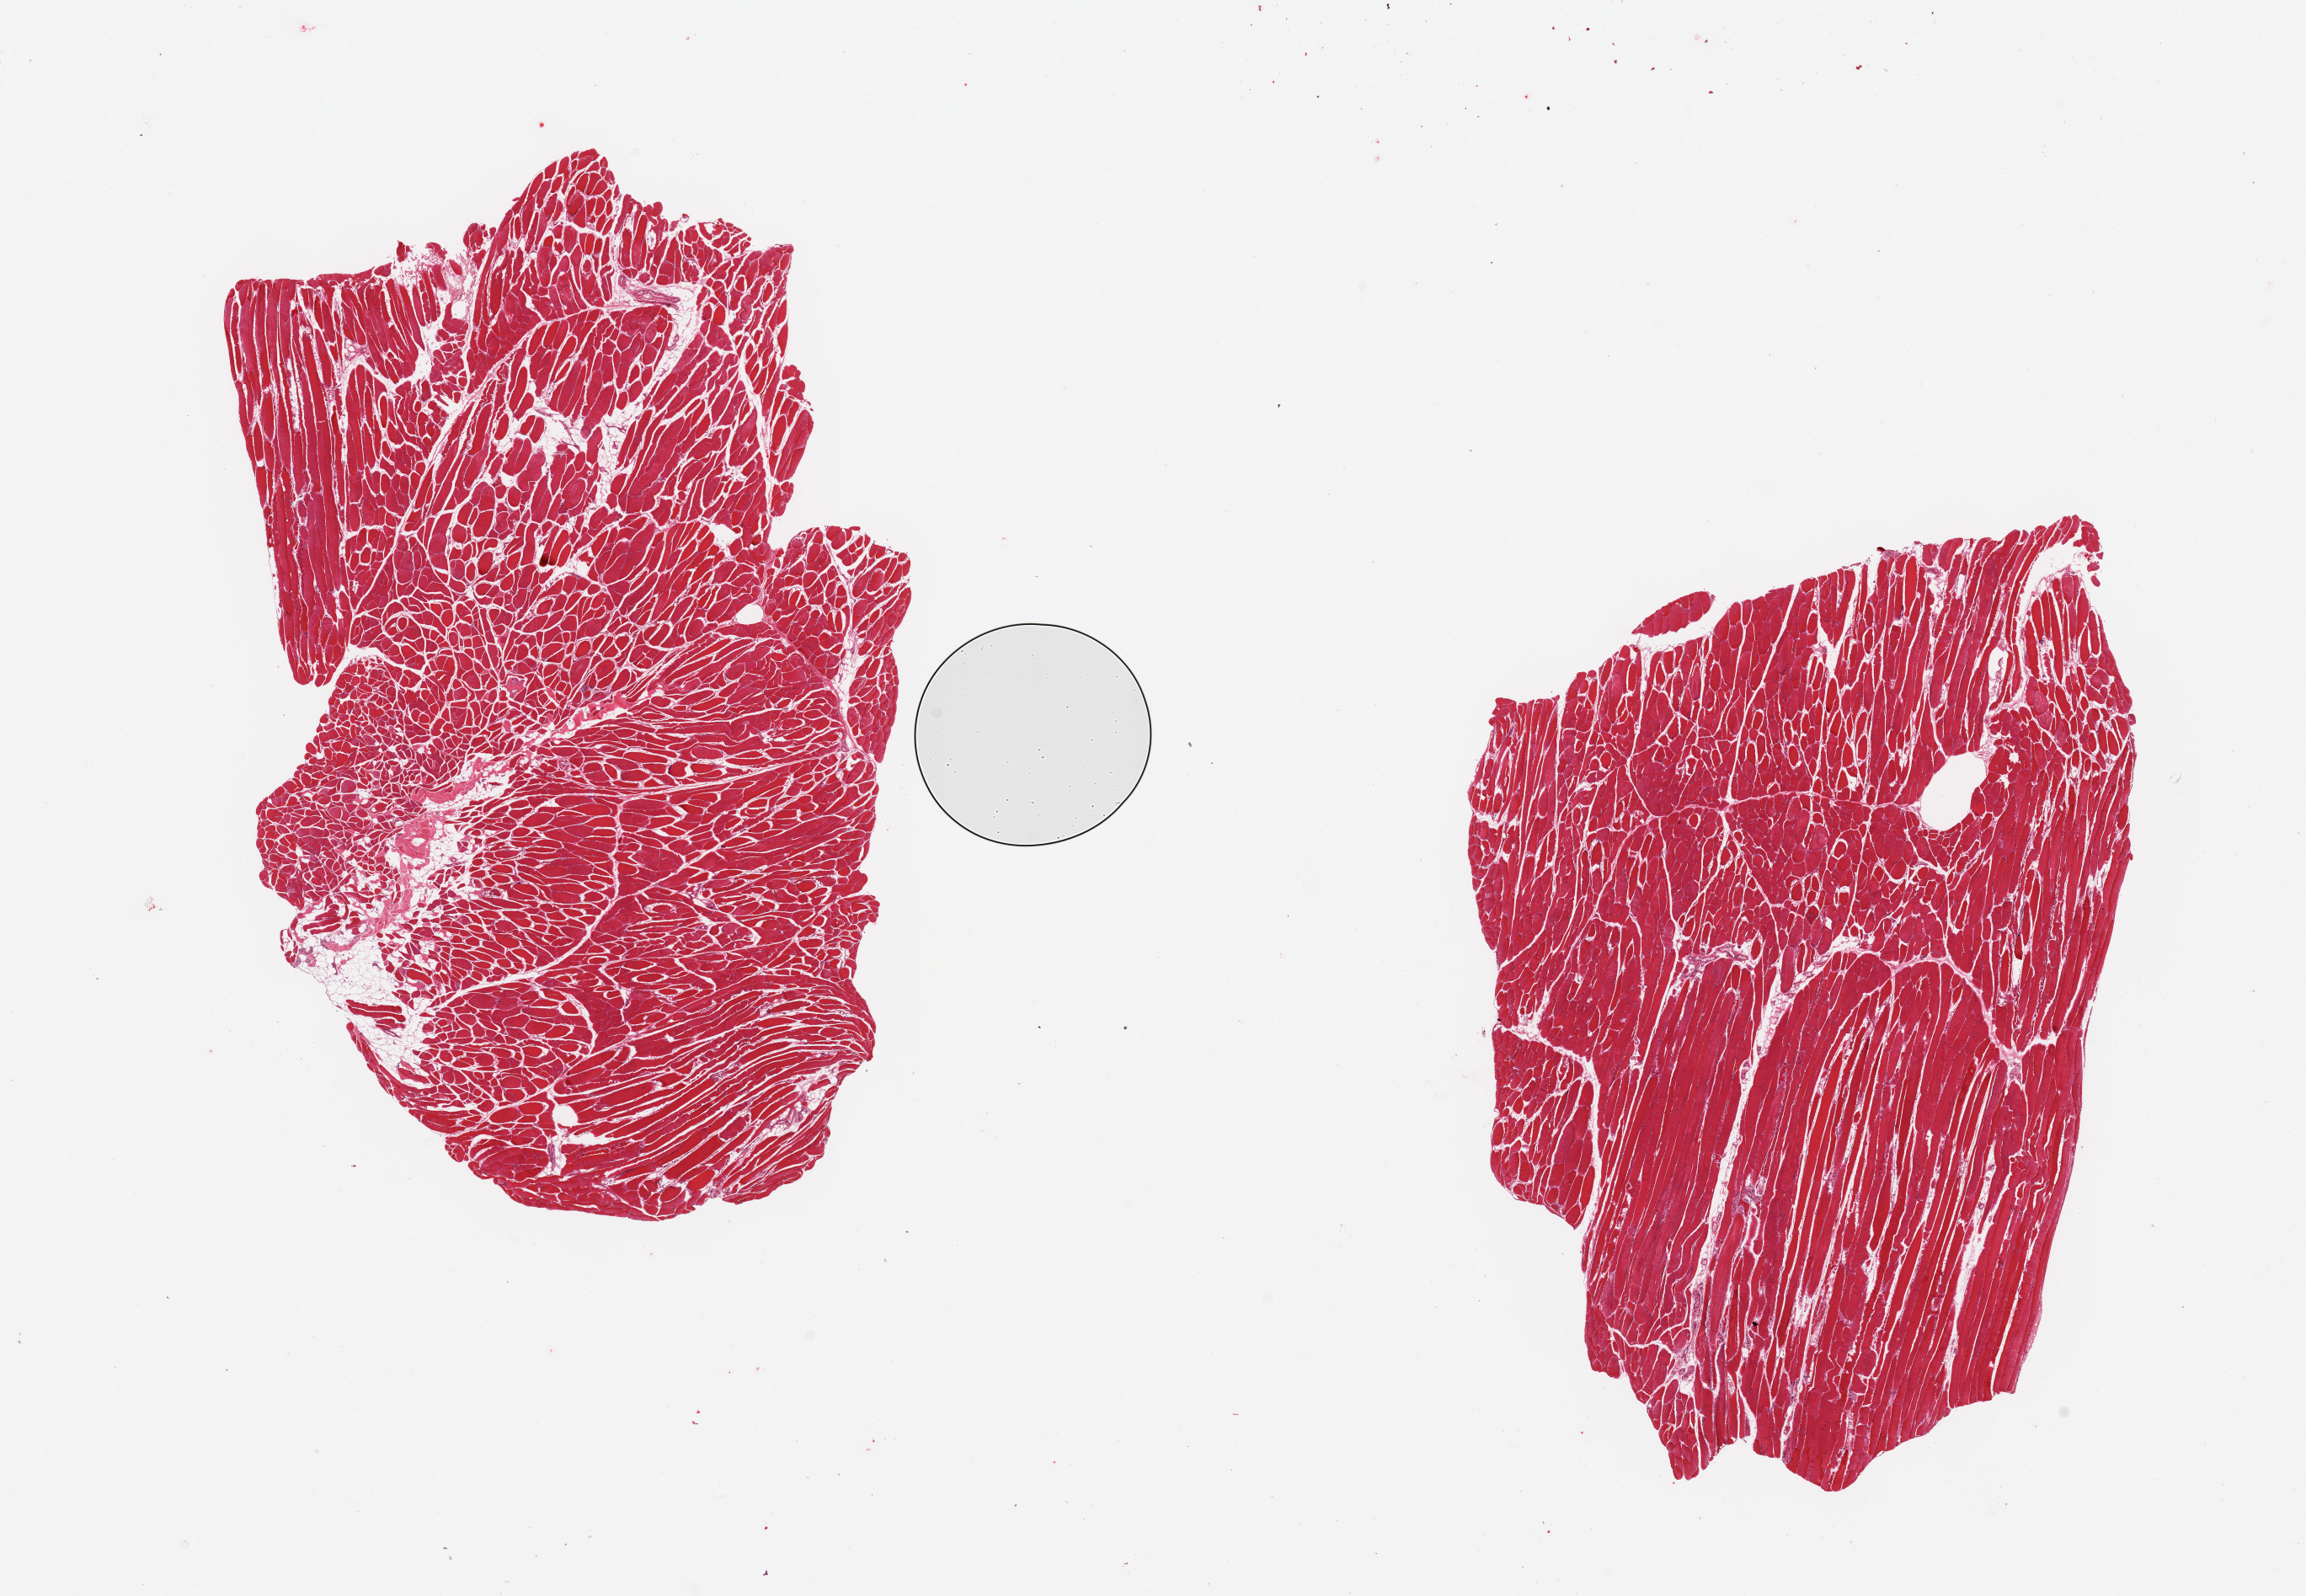
Haematoxylin and eosin whole-slide image, a low-resolution overview of the entire scanned area, about 21.7 x 15.0 mm, PAXgene-fixed, paraffin-embedded tissue, target tissue: skeletal muscle, tissue donor sample. Donor sex: male.
* reviewer comment on this tissue sample: 2 pieces